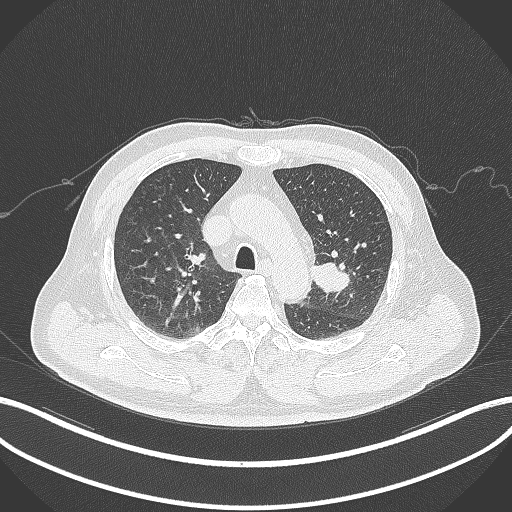
Chest CT, one axial slice; position 216 of 286 along the scan axis; lung window (W 1500 / L -600 HU); 512 × 512 image matrix, field of view 400 × 400 mm. Patient: male, 67 years. From the clinical record (not read from this slice): clinical TNM (as recorded): T2a N1 M0.
Annotated regions visible in this slice (bounding box drawn by a radiologist):
- lung tumour (recorded histology: adenocarcinoma): bounding box (x1, y1, x2, y2) in pixels: (307, 260, 357, 296)